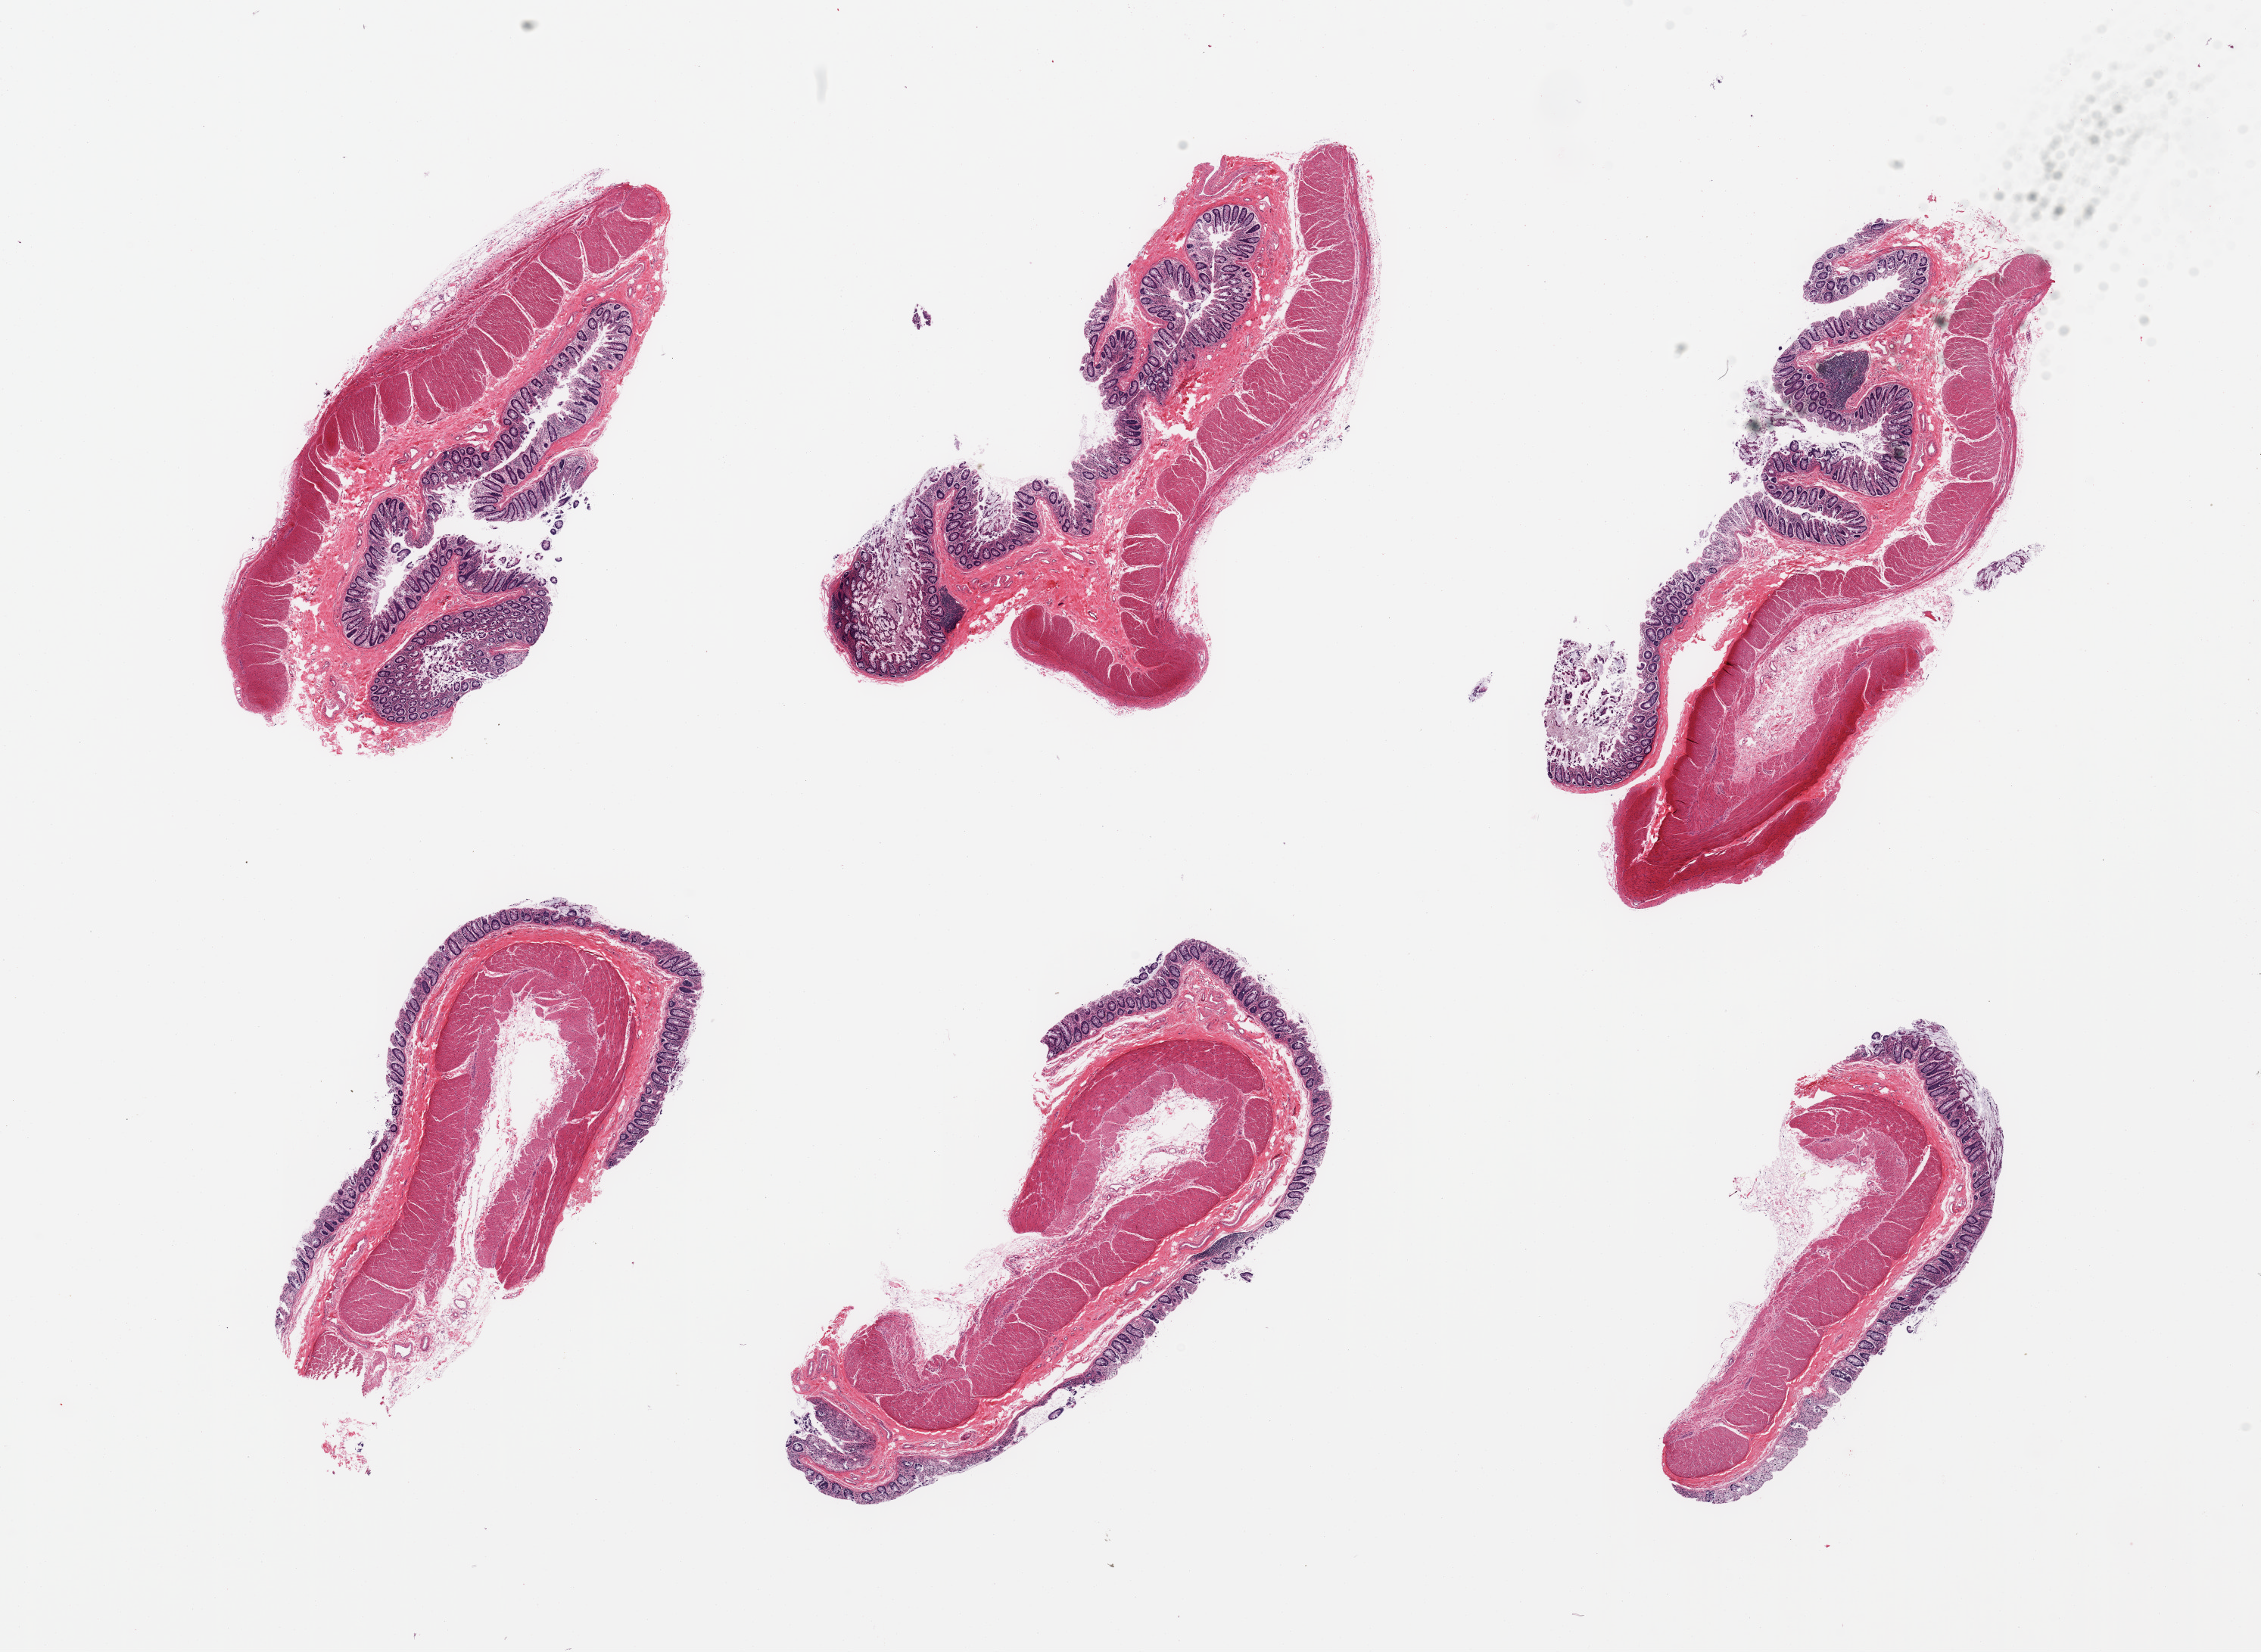
H&E whole-slide image — whole scanned area (about 23.6 x 17.3 mm) shown as a low-resolution overview; PAXgene-fixed, paraffin-embedded tissue; sampled site (target tissue): transverse colon; donor tissue sample.
Reviewer comment on this tissue sample: 6 pieces; mucosal autolysis varies from slight to severe.